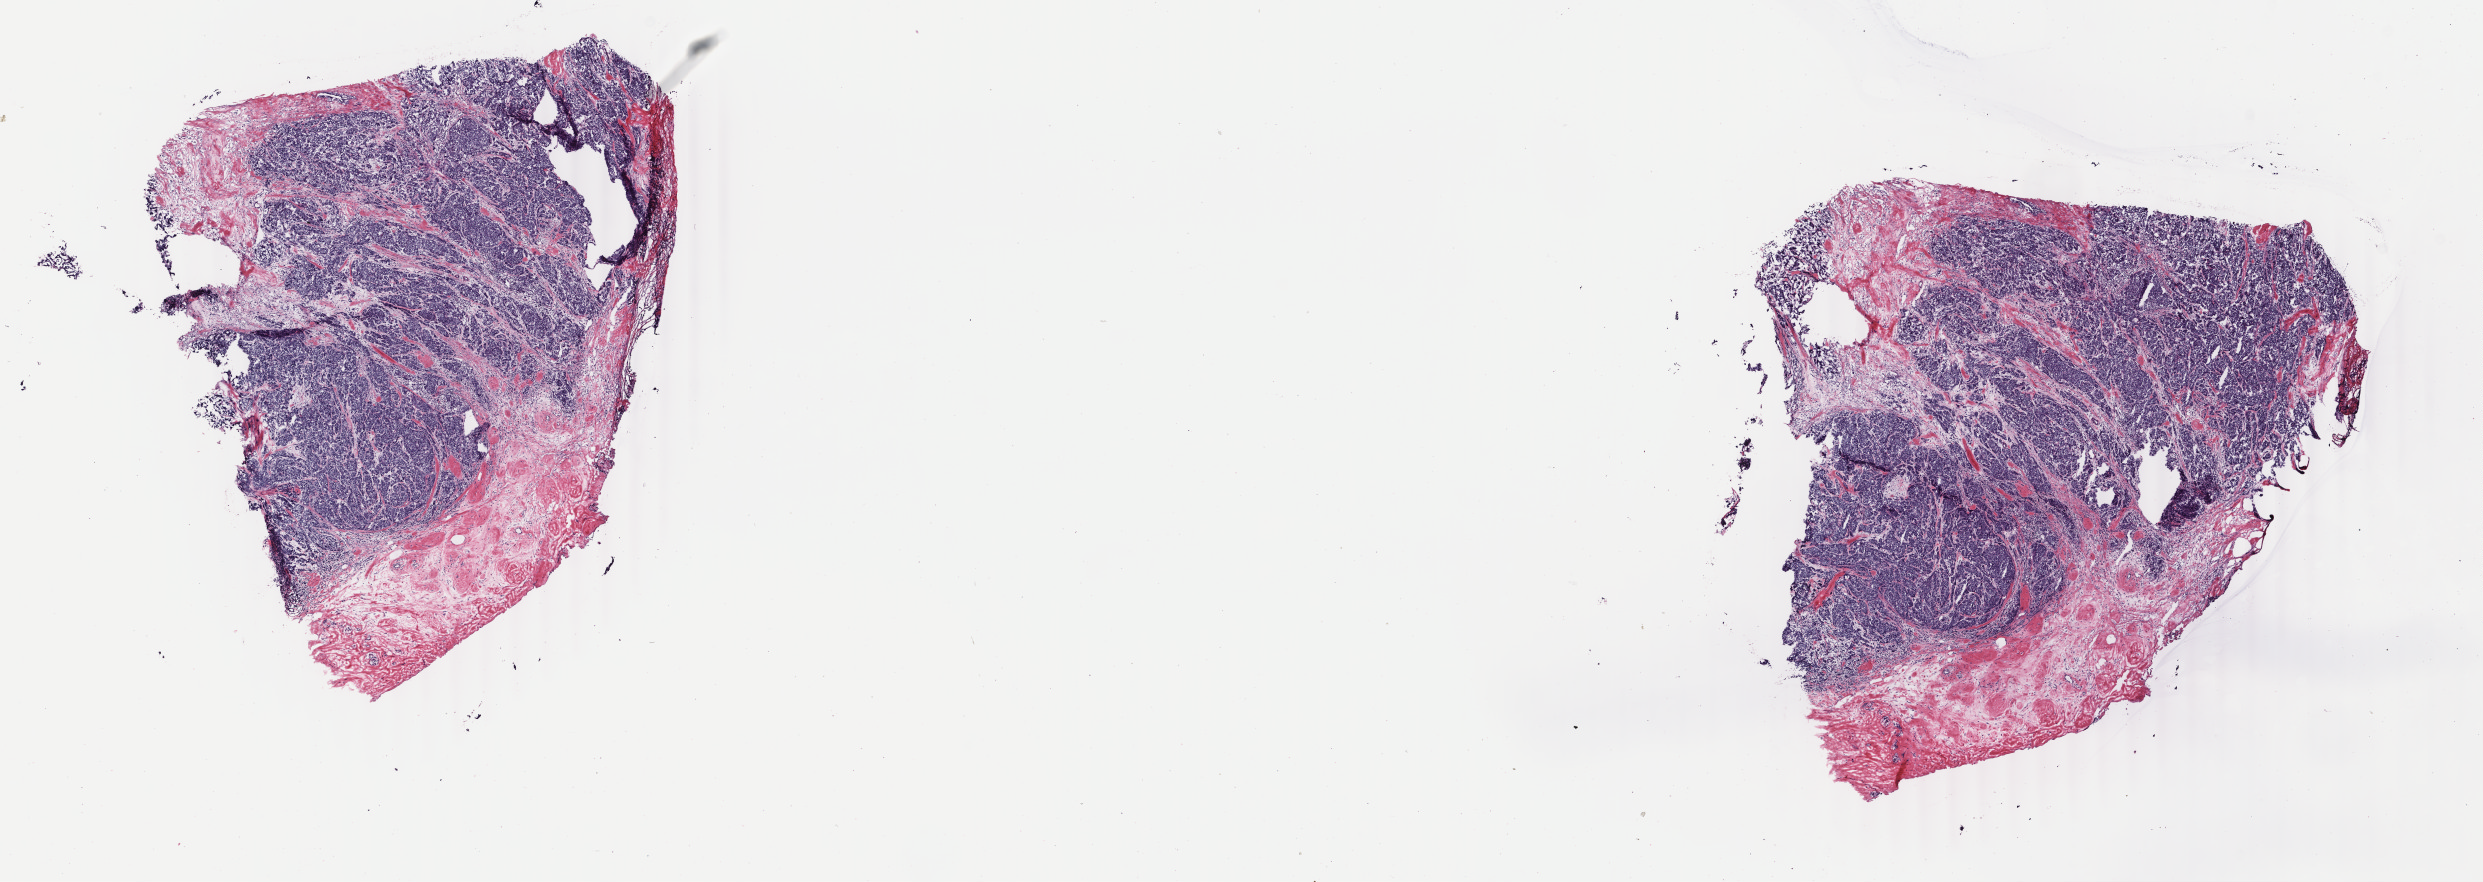
Hematoxylin and eosin (H&E) stained whole-slide image, whole scanned area (about 19.8 x 7.0 mm, acquisition: 40x scan) shown as a low-resolution overview; frozen section from the top of the tissue portion; breast, primary tumour sample. Female patient; age at initial diagnosis 47 years. Composition of this section per pathologist review: tumour cells 80%, tumour nuclei 90%, normal cells 0%, stromal cells 20%, necrosis 0%. Inflammatory infiltration, as recorded: lymphocyte infiltration 0%, monocyte infiltration 0%, neutrophil infiltration 0%.
Laterality: left. Lymph nodes positive (case pathology): 4 of 16 examined. Pathologic diagnosis: Infiltrating duct carcinoma, NOS. TNM: T2 N2 M0. AJCC pathologic stage: IIIA.